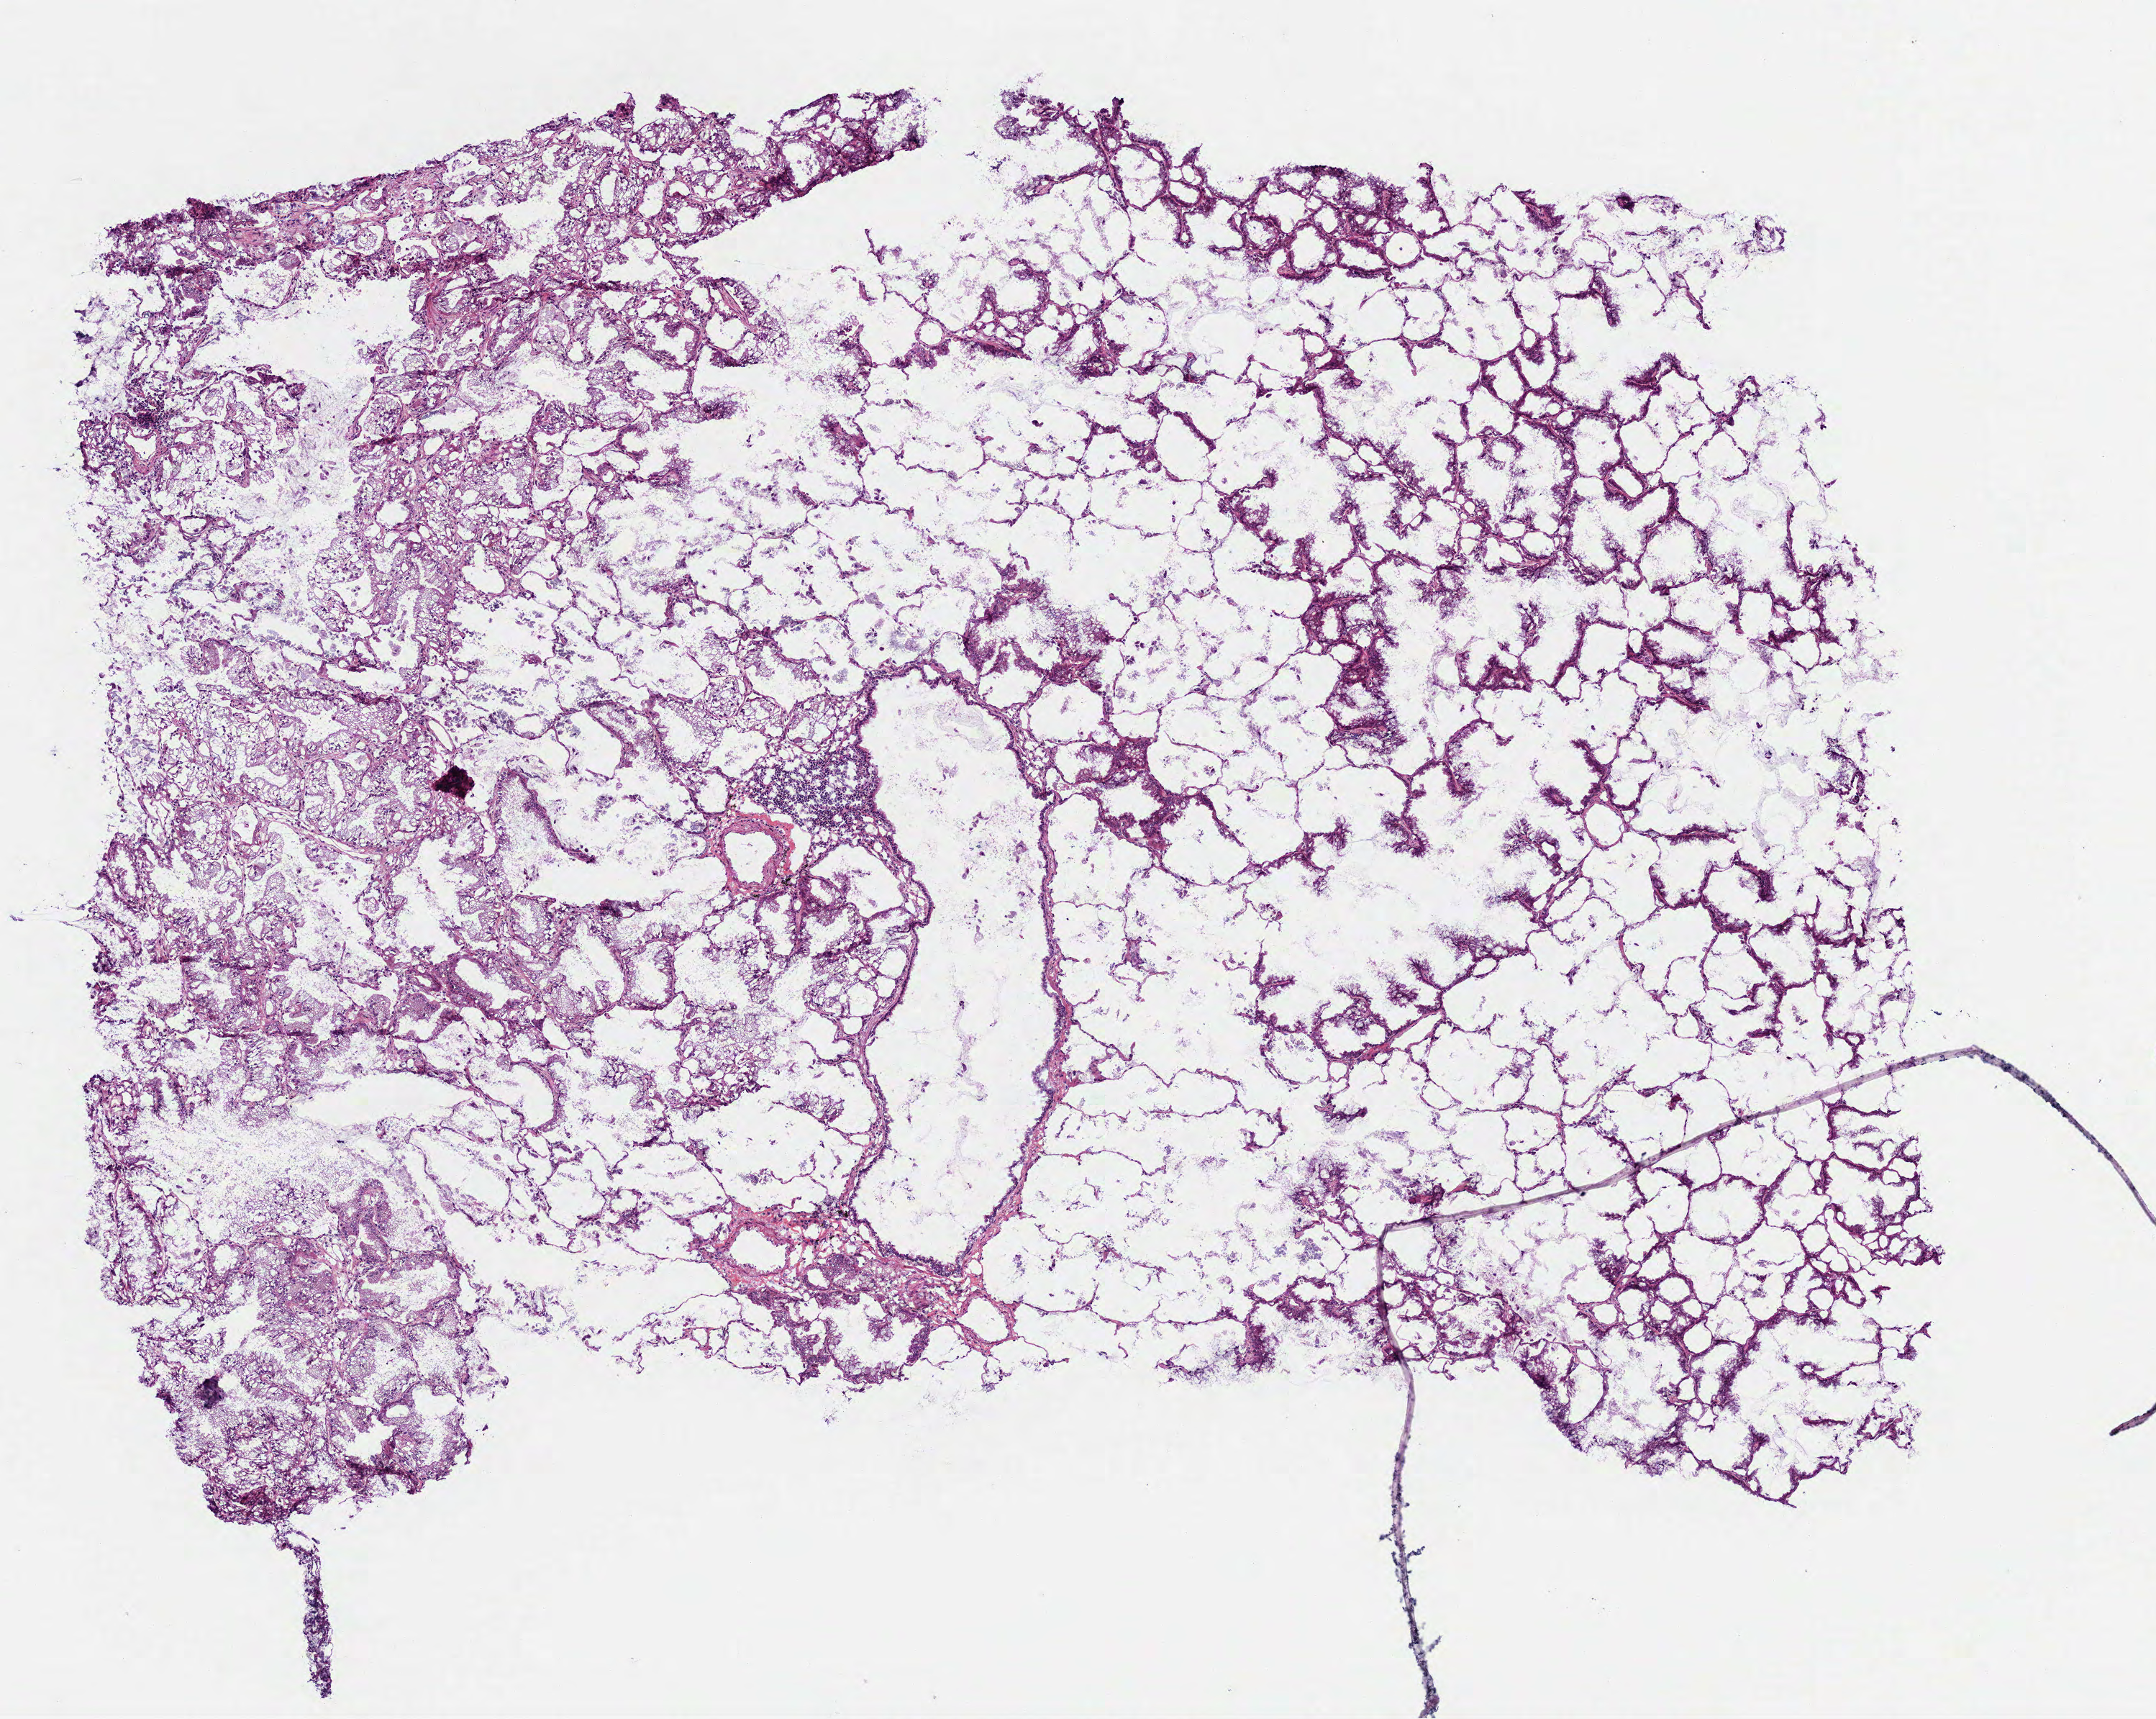
Whole-slide histology image, Hematoxylin and eosin (H&E) stained — whole scanned area (about 6.0 x 4.8 mm, from a 40x scan) shown as a low-resolution overview, frozen section from the bottom of the tissue portion, sample: primary tumour, lung. Patient: female, age at initial diagnosis 66 years. Pathologist review of this section (percent, as recorded): tumour cells 100%, tumour nuclei 85%, normal cells 0%, stromal cells 0%, necrosis 0%. Inflammatory infiltration, as recorded: lymphocyte infiltration 2%, monocyte infiltration 2%, neutrophil infiltration 0%.
• pathologic diagnosis: Bronchio-alveolar carcinoma, mucinous (lower lobe, lung)
• TNM: T2 N0 M0
• AJCC pathologic stage: IB